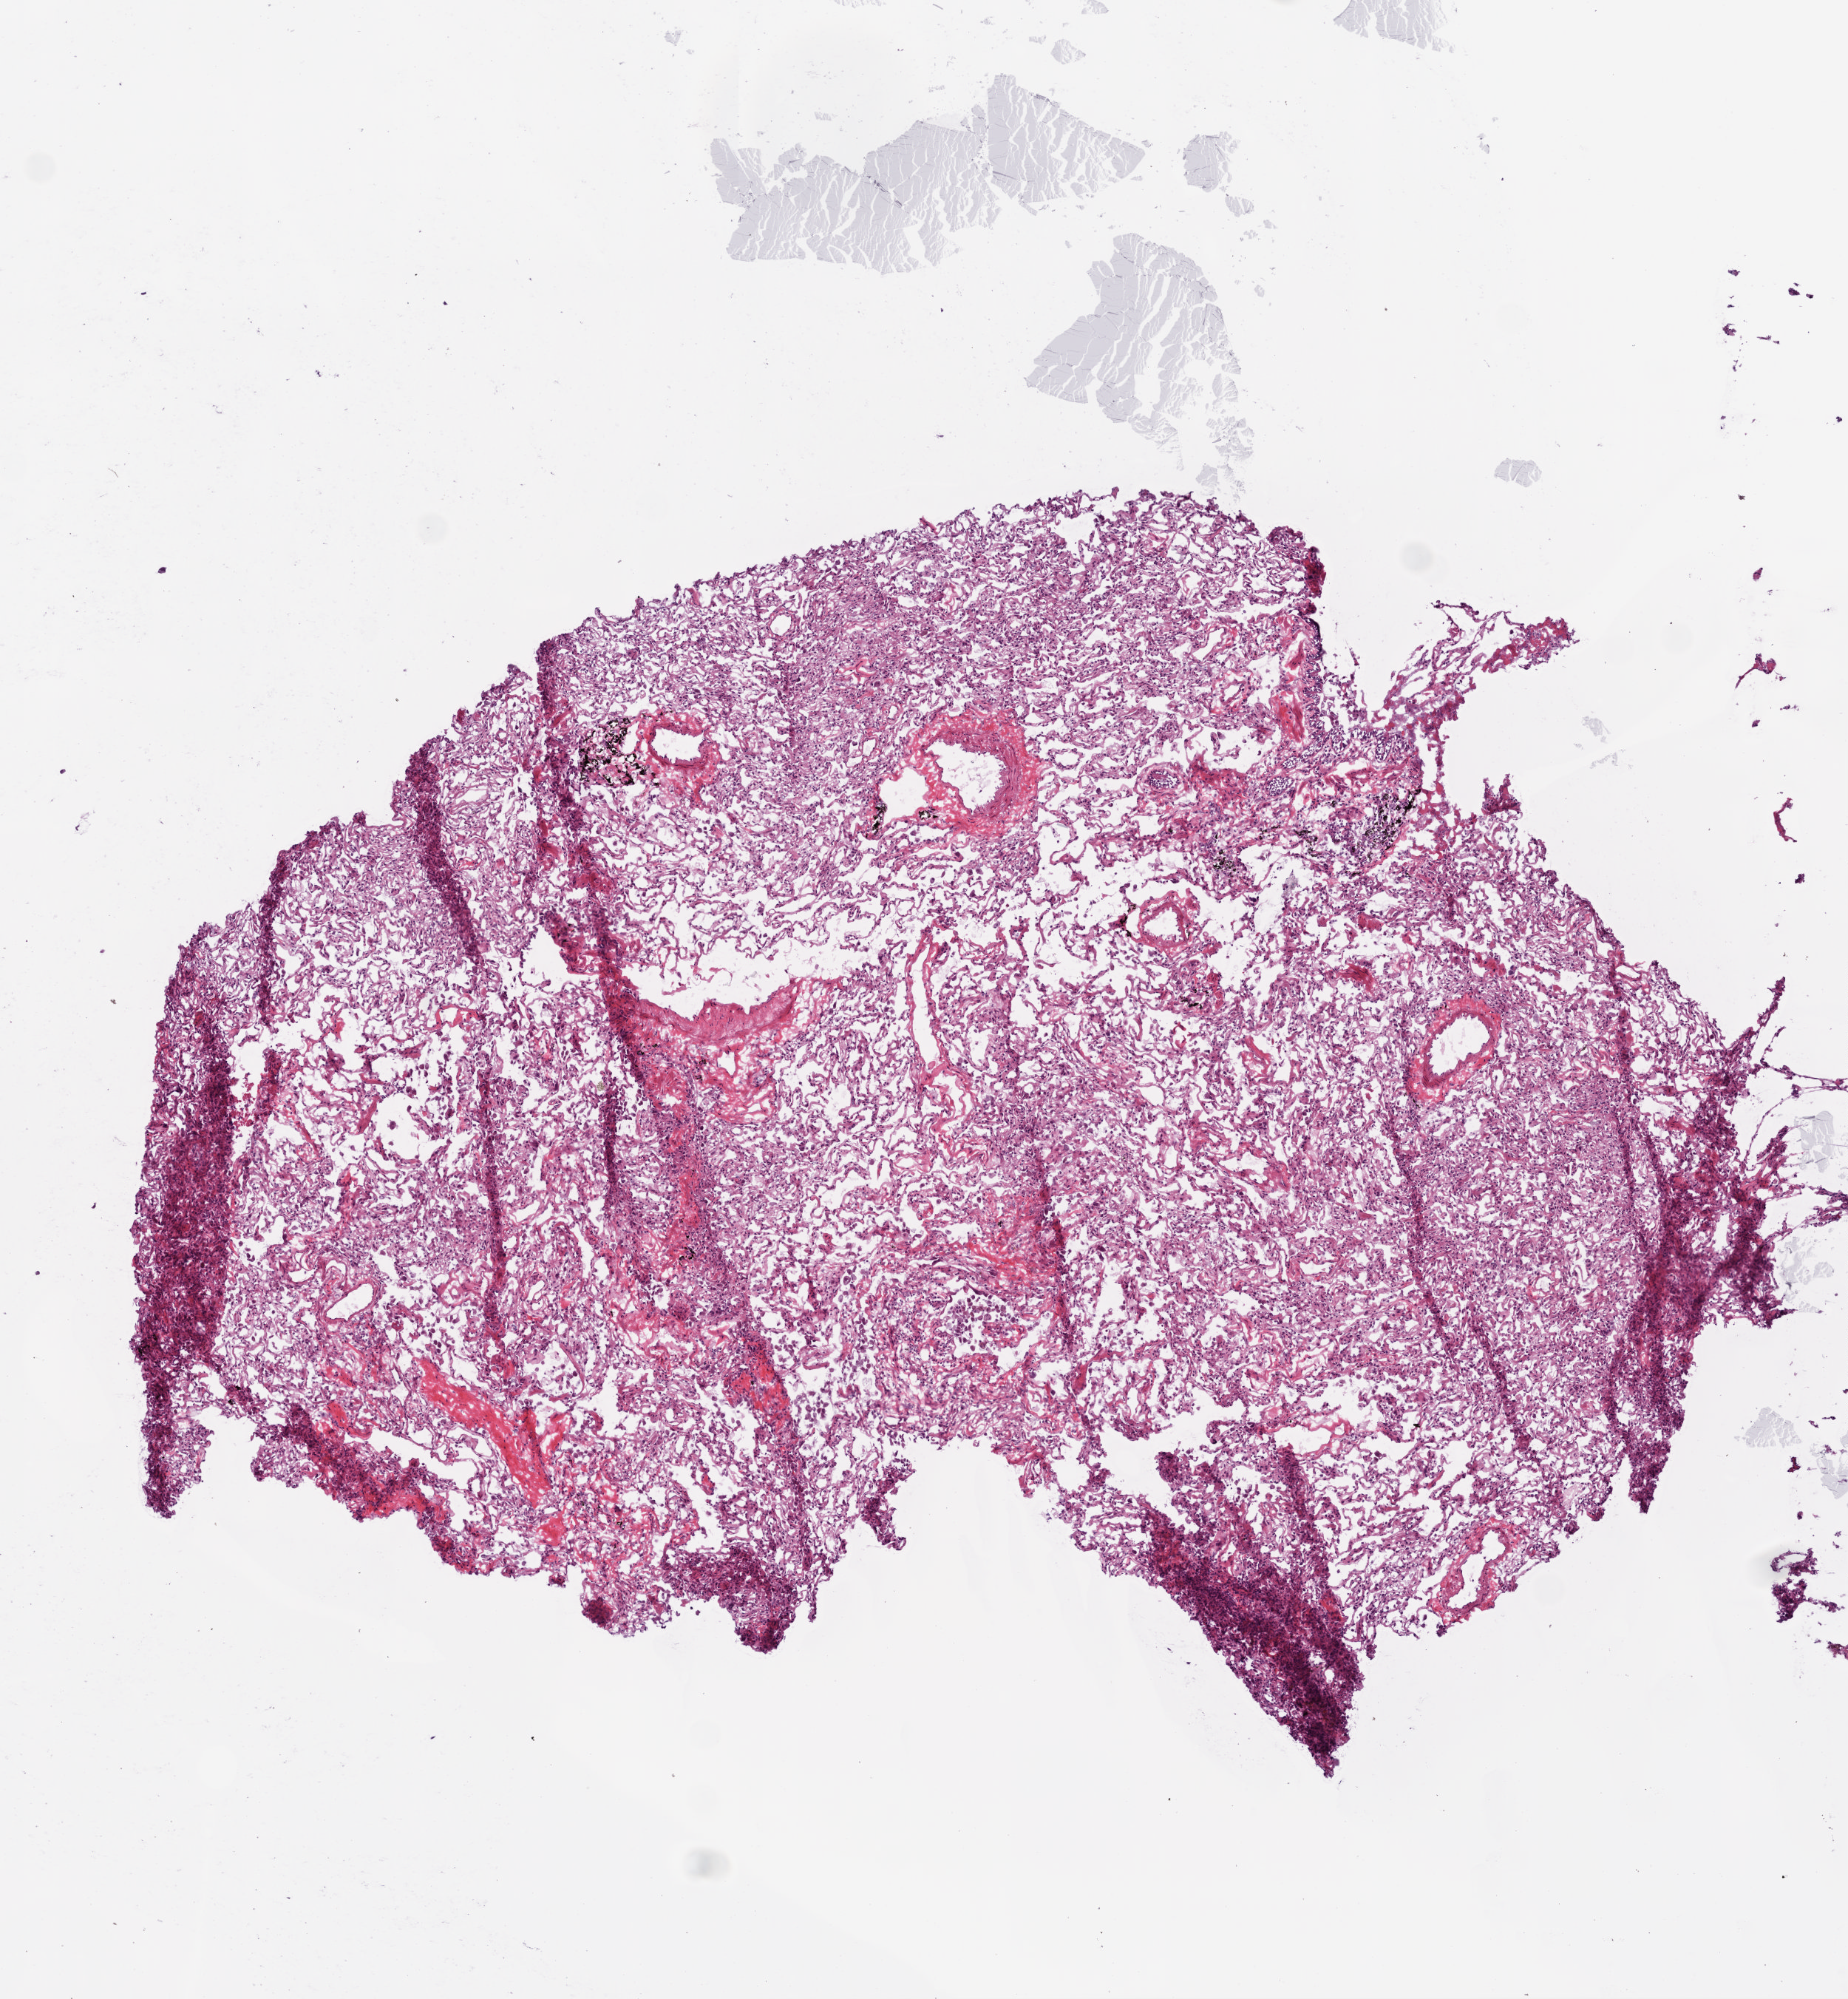
Digitized Hematoxylin and eosin (H&E) stained tissue section (whole slide), whole scanned area (about 5.0 x 5.4 mm) shown as a low-resolution overview; frozen section from the top of the tissue portion; solid tissue normal (non-tumour tissue) sample from the lung. Male patient; age at initial diagnosis 64 years.
This section: solid tissue normal sample (biorepository sample class). Patient diagnosis: Squamous cell carcinoma, NOS (lower lobe, lung).